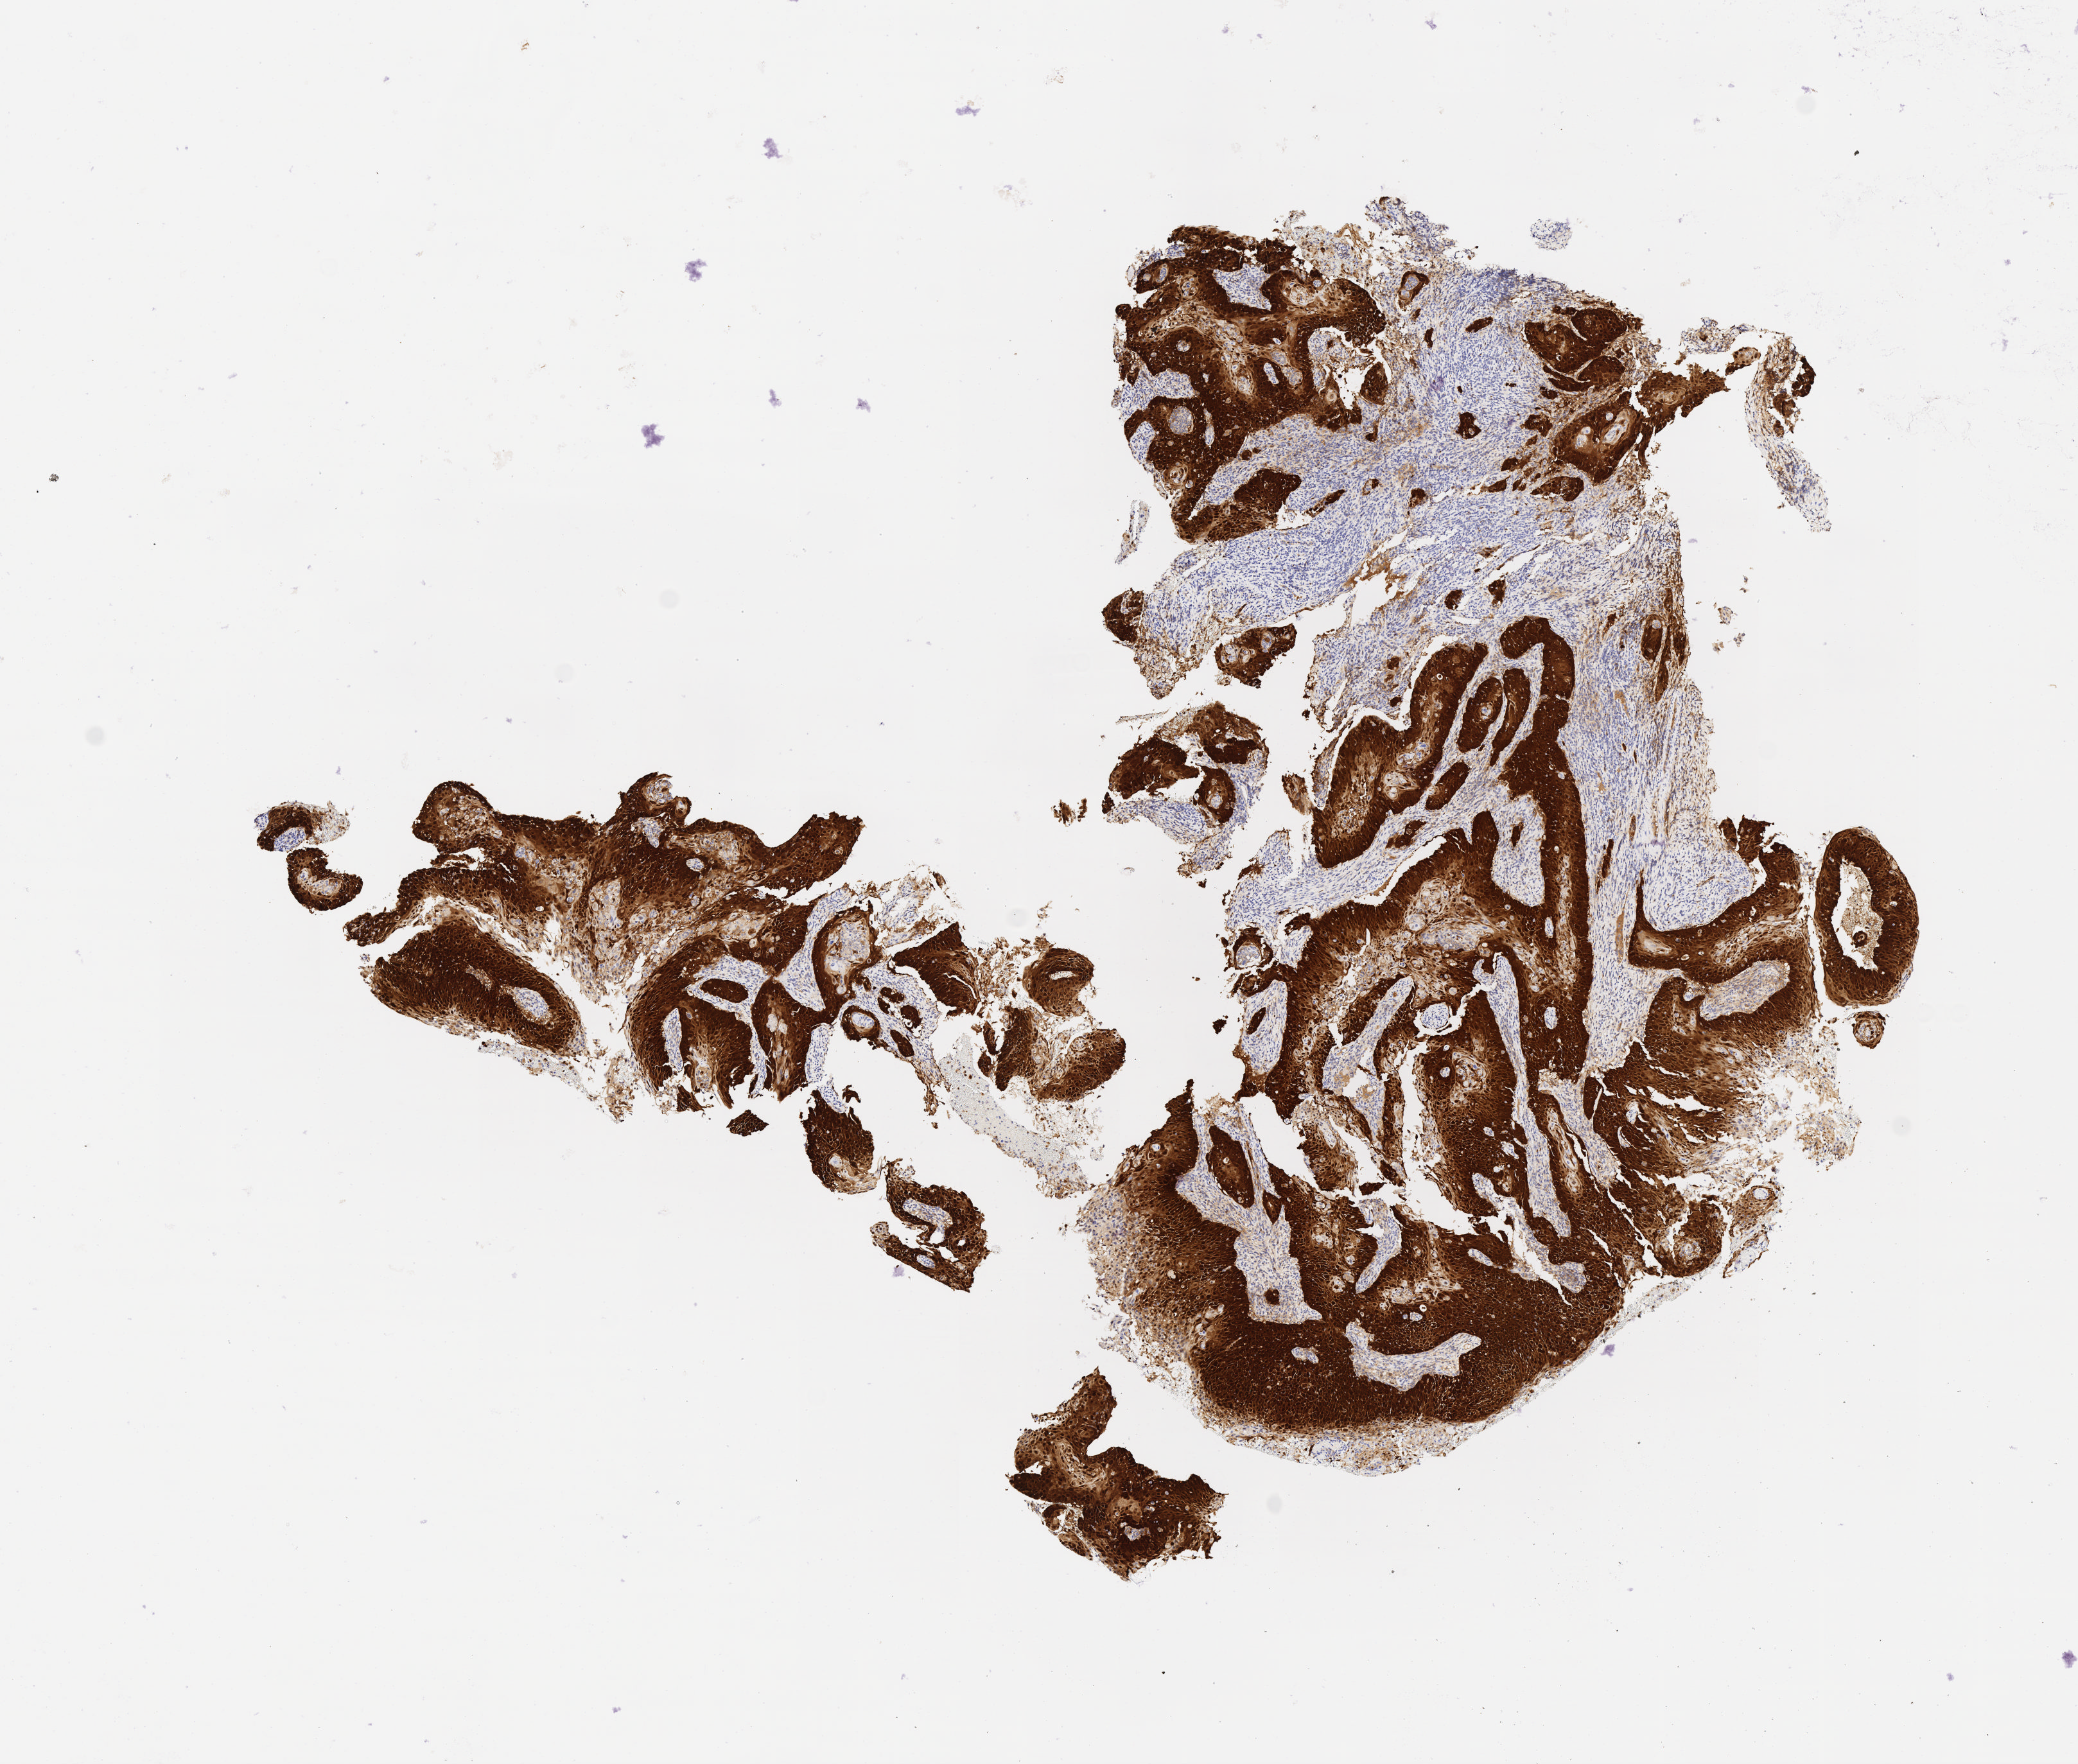
IHC for p16 (p16INK4a), whole-slide image — low-resolution overview of the scanned area, about 6.5 x 5.6 mm; specimen: tumor tissue; site: cervix. Patient female; aged 60.
Histologic diagnosis: Squamous cell carcinoma, keratinizing, NOS.